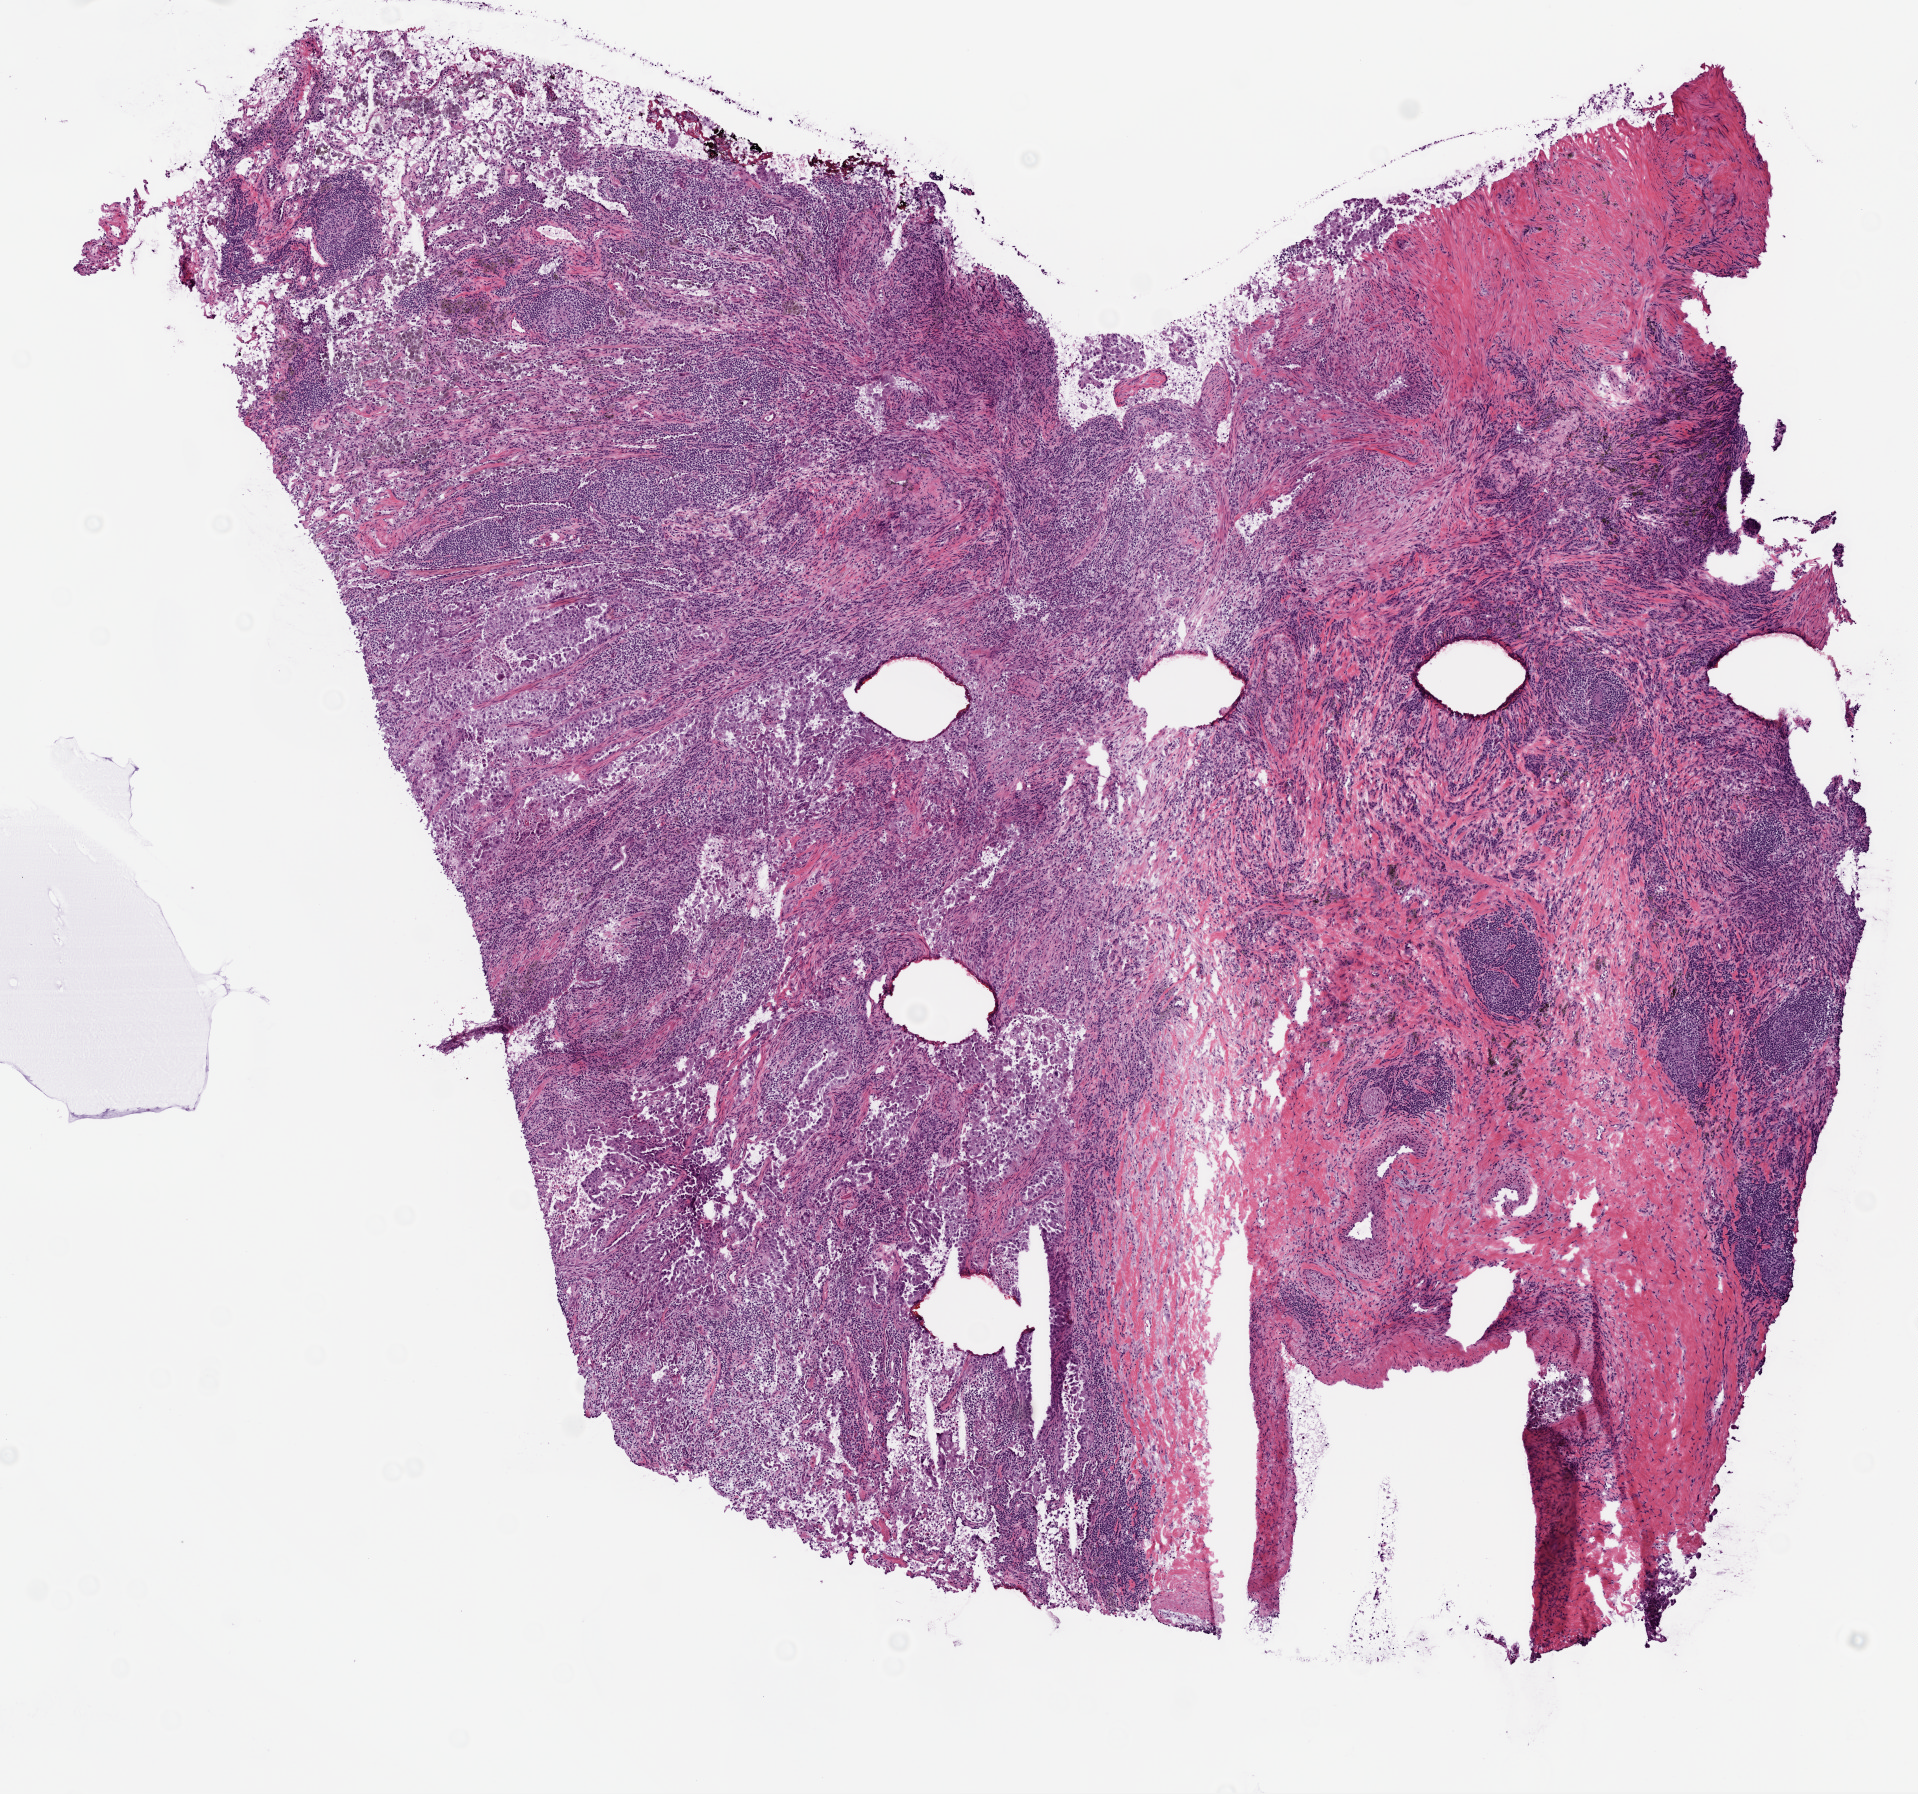
H&E-stained whole-slide image — shown as a low-resolution overview of the whole scanned area (about 7.7 x 7.2 mm, acquisition: 20x scan). Frozen section. Primary tumour sample from the lung. Female, age 52 years at initial diagnosis. Composition of this section per pathologist review: tumour cells 100%, tumour nuclei 60%, necrosis 0%. Inflammatory infiltration, as recorded: lymphocyte infiltration 30%, monocyte infiltration 3%, neutrophil infiltration 3%.
* histologic diagnosis: Adenocarcinoma, NOS (upper lobe, lung)
* TNM: T1b N0 M0
* AJCC pathologic stage: IA (7th edition)